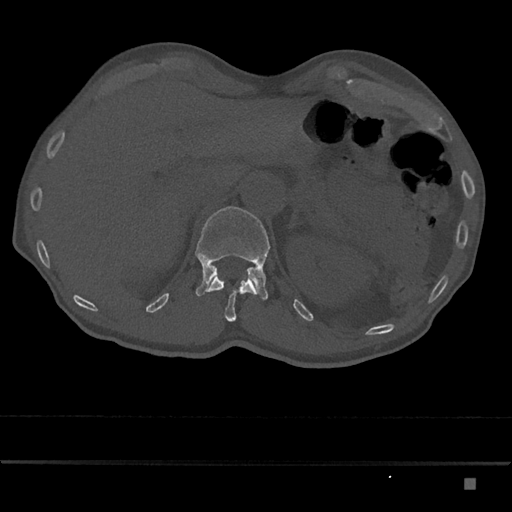
CT including the spine, one axial slice. Slice 577 of 797 in the series (ordered by position). 120 kVp. Bone window (W 1800 / L 400 HU). 512 × 512 image matrix, field of view 390 × 390 mm. Patient: male, 72 years. From the clinical record (not read from this slice): primary cancer: prostate.
Annotated regions visible in this slice (semi-automatic segmentation, software-assisted and operator-edited):
- L1 vertebra: bounding box [x1, y1, x2, y2] px = [195, 206, 270, 300]
- T12 vertebra: [205, 275, 257, 322]